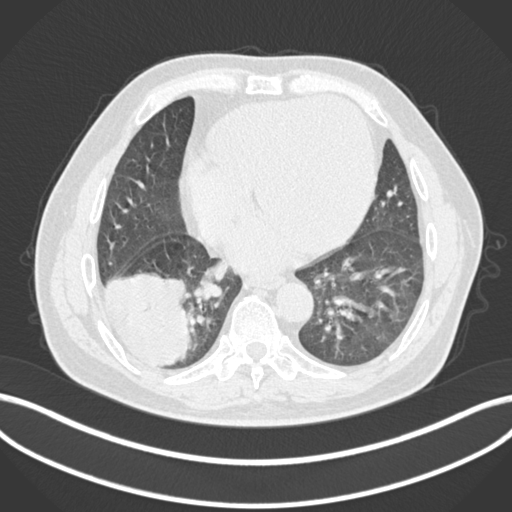
Chest CT, one axial slice; reconstruction kernel B30f; 120 kVp; lung window (W 1500 / L -600 HU); 512 × 512 image matrix. Male patient, age 59 years.
Structures marked on this image (bounding box drawn by a radiologist):
- lung tumour (recorded histology: adenocarcinoma): bounding box (x1, y1, x2, y2) in pixels: (100, 268, 195, 367)